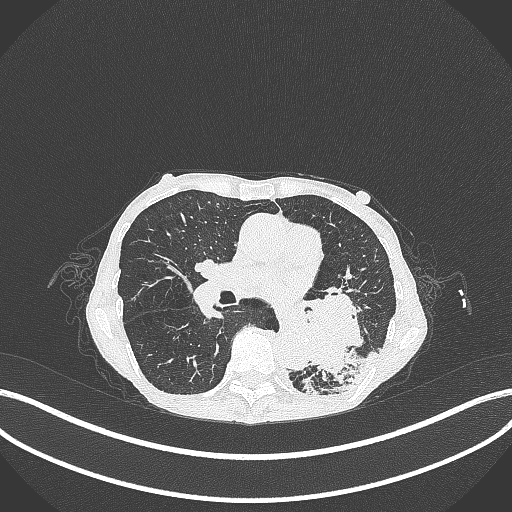
Chest CT, one axial slice. Slice 140 of 347 in the series (ordered by position). Reconstruction kernel B70f. 120 kVp. Lung window (W 1500 / L -600 HU). 512 × 512 image matrix, field of view 400 × 400 mm. Patient: female, 70 years. Case-level facts recorded for this patient, not image findings: clinical TNM (as recorded): T3 N0 M0.
Structures marked on this image (rectangle marked by the reading radiologist):
- lung tumour (recorded histology: small cell carcinoma): bounding box (x1, y1, x2, y2) in pixels: (294, 294, 374, 389)